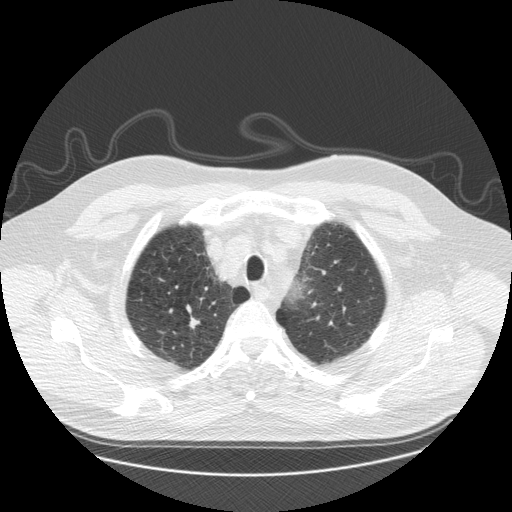
Chest CT (low-dose screening protocol), one axial image, third screening round (two years after baseline), lung window (W 1500 / L -600 HU), 2.5 mm slice thickness, slice 28 of 173 in the series. Male, age 61 years at enrolment. Former smoker at enrolment.
• Expert-annotated lung lesion, bounding box (x1, y1, x2, y2) in pixels: (175, 305, 211, 339).
• Reader record for this screening exam (exam-level; its link to the box is not recorded): non-calcified nodule or mass ≥4 mm, right upper lobe, 10 × 7 mm, smooth margins, soft tissue attenuation, pre-existing on the prior screen: yes; interval growth: yes.
• Participant outcome: lung cancer diagnosed 110 days after this screen — squamous cell carcinoma, NOS, right upper lobe, moderately differentiated (G2), stage IA (AJCC 6th edition), 10 mm at pathology.